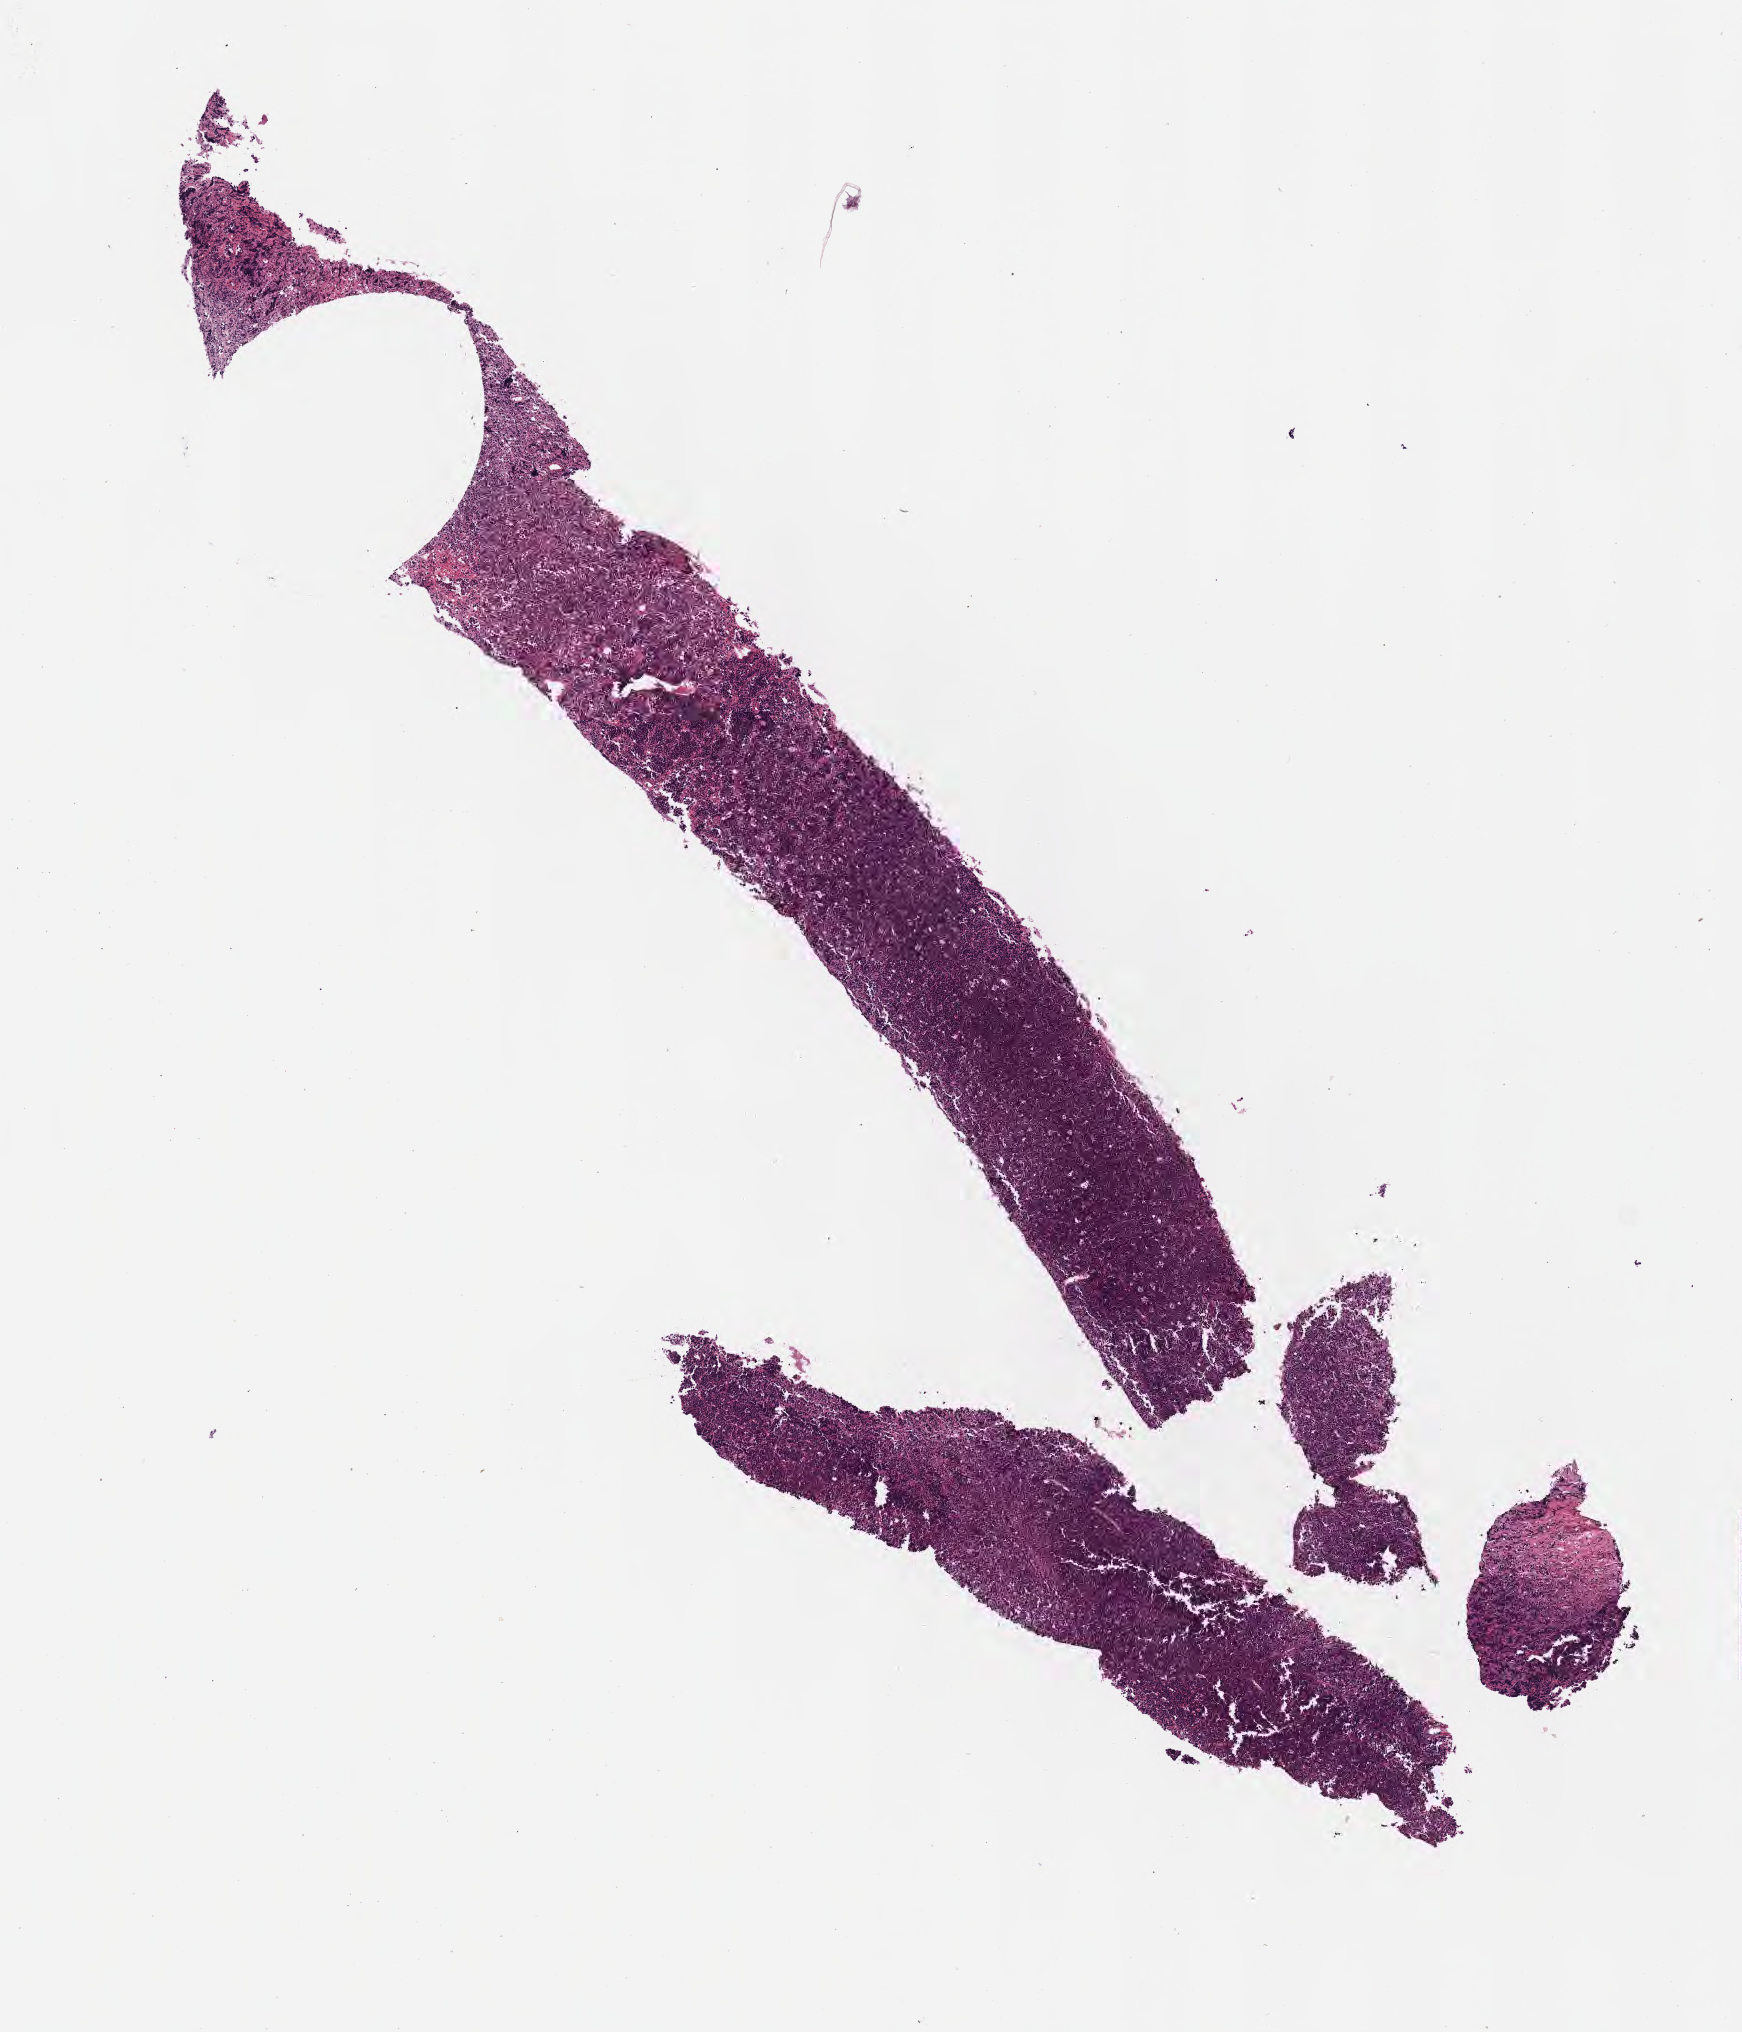
Whole-slide image, hematoxylin and eosin (H&E) stain — shown as a low-resolution overview of the whole scanned area (about 7.0 x 8.2 mm), tumor tissue, anatomic site: liver. Patient male; aged 15.
Diagnosis: Burkitt lymphoma, NOS.